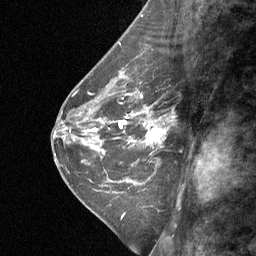
Breast MRI (dynamic contrast-enhanced), one sagittal slice. Slice 25 of 64 in the series (ordered by position). Dynamic contrast-enhanced study with each time point stored as its own series, time point 2 of 3 at this slice position (early post-contrast, ordered by acquisition time). 1.5 T. TE 4.8 ms, TR 27 ms. 2 mm slice thickness. 256 × 256 image matrix, field of view 180 × 180 mm. Female patient, age 42 years. From the clinical record (not read from this slice): setting: breast cancer imaged before/during neoadjuvant chemotherapy; receptor status: triple-negative.
Structures marked on this image (semi-automatic segmentation, software-assisted and operator-edited):
- analysis volume of interest (the breast-tissue region the enhancement analysis was run in; not a lesion): box from (x=124, y=94) to (x=170, y=161) px
- tumour enhancement mask (voxels above the 90 % enhancement threshold inside the analysis volume of interest): (x=134, y=108)–(x=166, y=144)